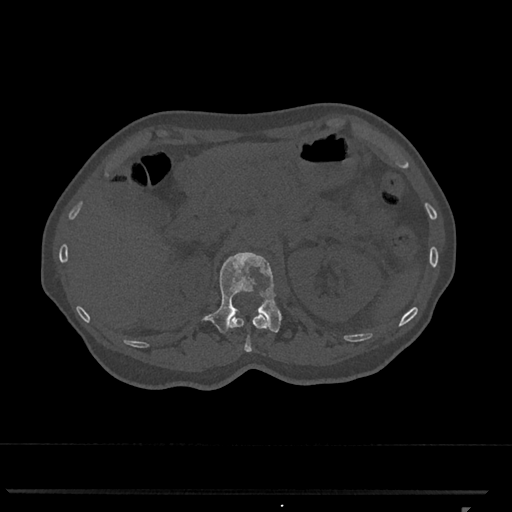
CT including the spine, one axial slice. Slice 421 of 793 in the series (ordered by position). Reconstruction kernel Br40s/3. Bone window (W 1800 / L 400 HU). 512 × 512 image matrix. Patient: female, 62 years. From the clinical record (not read from this slice): primary cancer: renal.
Structures marked on this image (semi-automatic segmentation, software-assisted and operator-edited):
- L1 vertebra: box from (x=202, y=252) to (x=282, y=333) px
- T12 vertebra: (x=229, y=312)–(x=267, y=352)